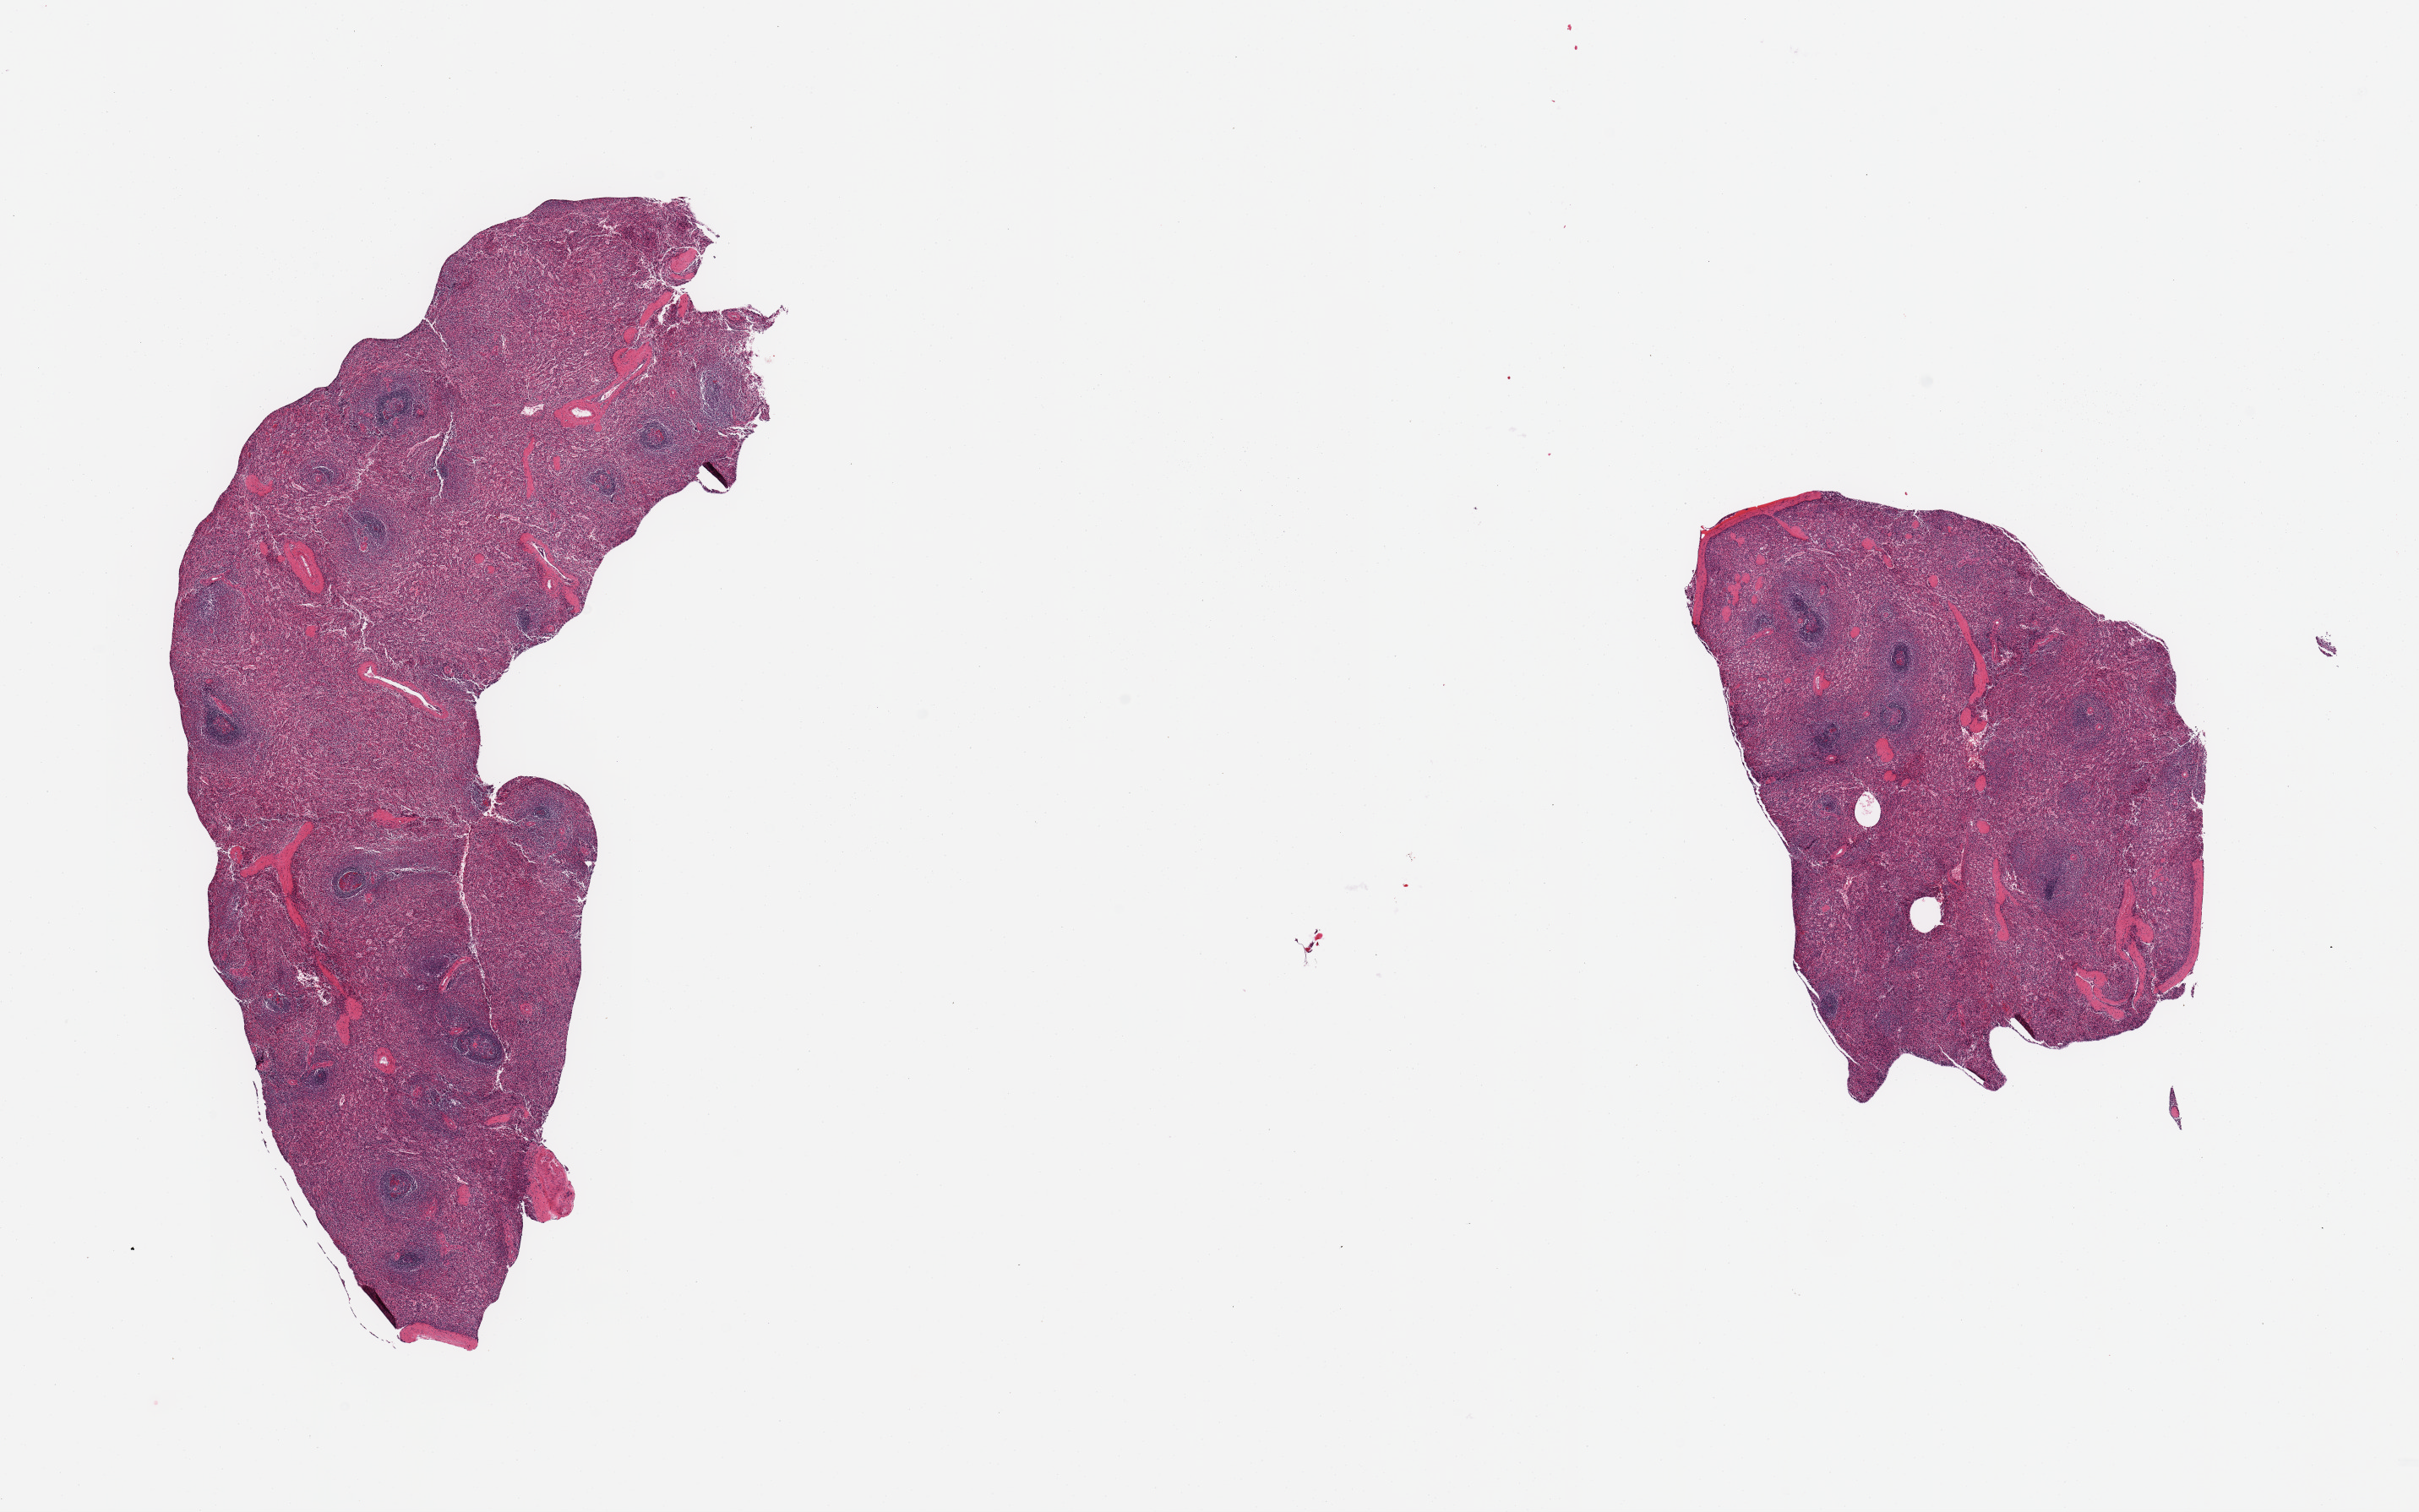
Digitized hematoxylin and eosin (H&E)-stained section — whole scanned area (about 22.6 x 14.2 mm) shown as a low-resolution overview; PAXgene-fixed paraffin-embedded (PFPE) section; section of spleen (target tissue); donor tissue sample. Donor sex: female.
Pathologist's review note for this sample: 2 pieces; marked congestion.